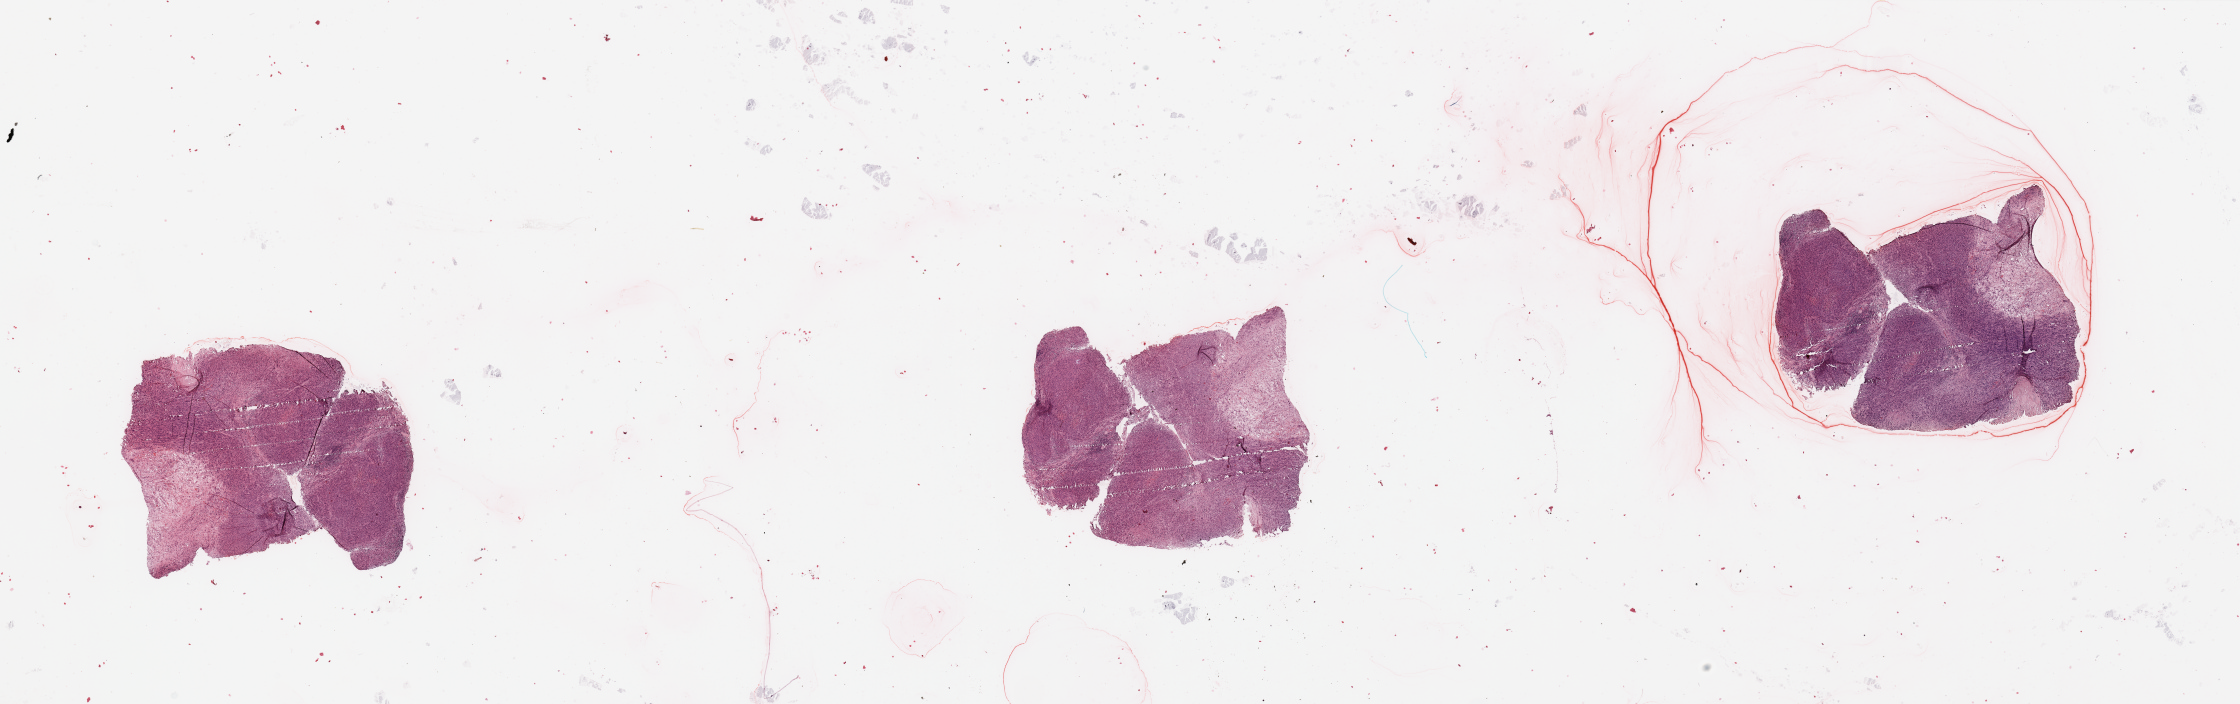
Whole-slide histology image, H&E-stained, shown as a low-resolution overview of the whole scanned area (about 35.4 x 11.1 mm, from a 20x scan). Tumour tissue sample, sampled site: lymph node. Patient: male, age 84 years. Pathologist review of this section (percent, as recorded): tumour nuclei 90%, necrosis 0%.
This section: metastatic tumour tissue. Patient diagnosis: Malignant melanoma, NOS.